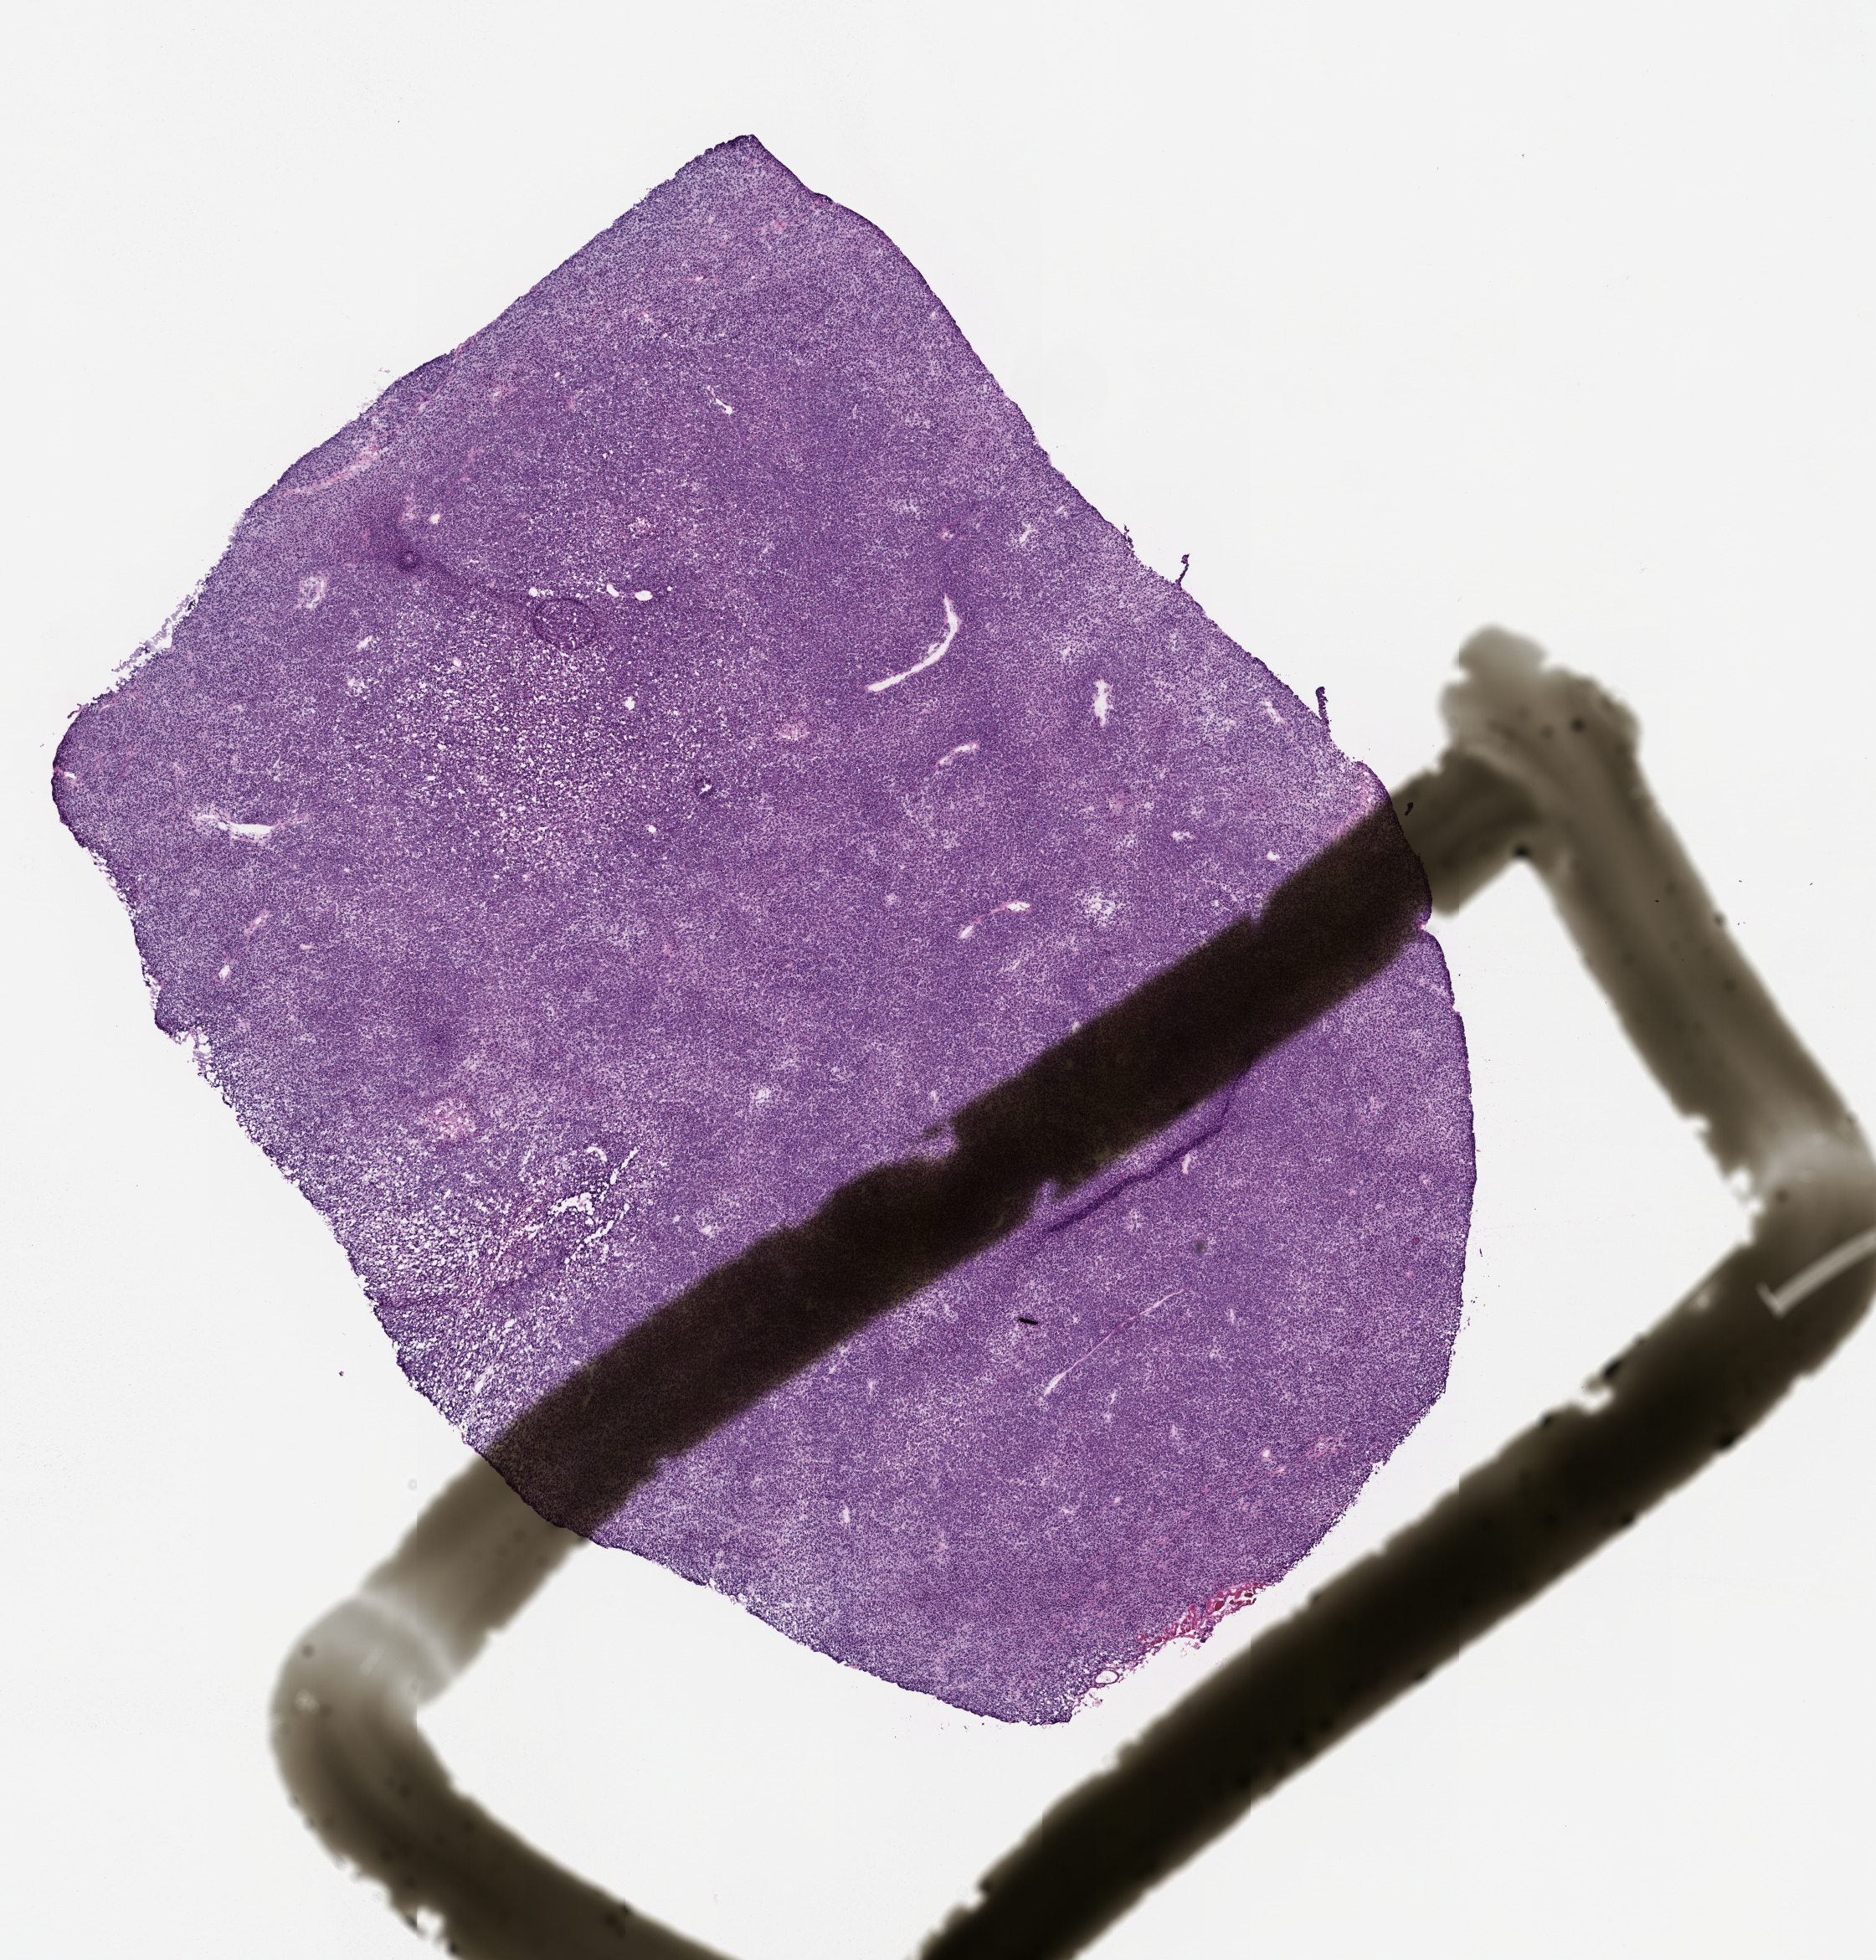
Whole-slide image, haematoxylin and eosin: patient-derived xenograft (human tumor grown in a mouse) — whole scanned area (about 9.0 x 9.4 mm) shown as a low-resolution overview; formalin-fixed, paraffin-embedded (FFPE) tissue; tumor site category: skin.
* originating patient diagnosis: Melanoma